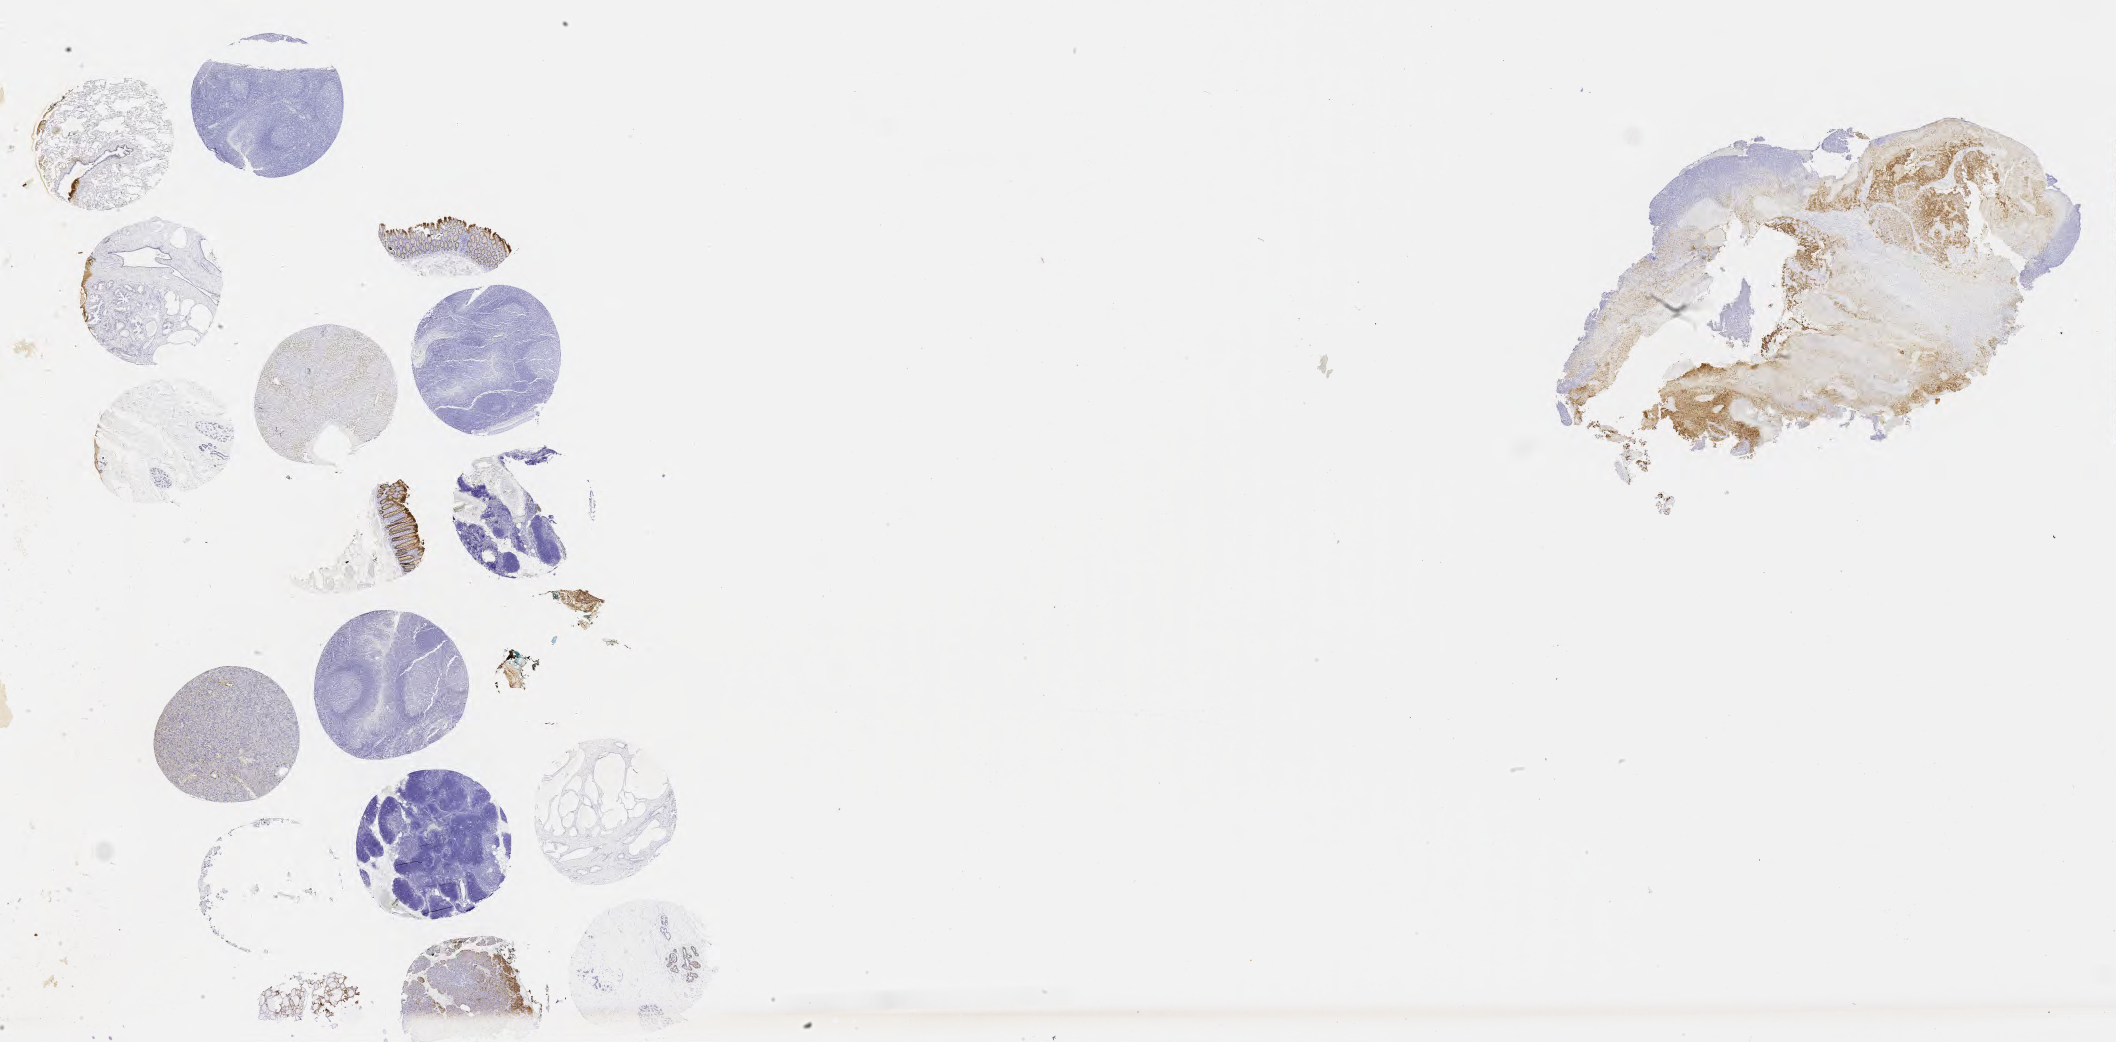
Whole-slide image, immunohistochemical stain for MOC-31 (anti-EpCAM), a low-resolution overview of the entire scanned area, about 34.2 x 16.8 mm; specimen: tumor tissue; site: cervix. Patient: female, age 62 years.
Histologic diagnosis: Squamous cell carcinoma, large cell, nonkeratinizing, NOS.